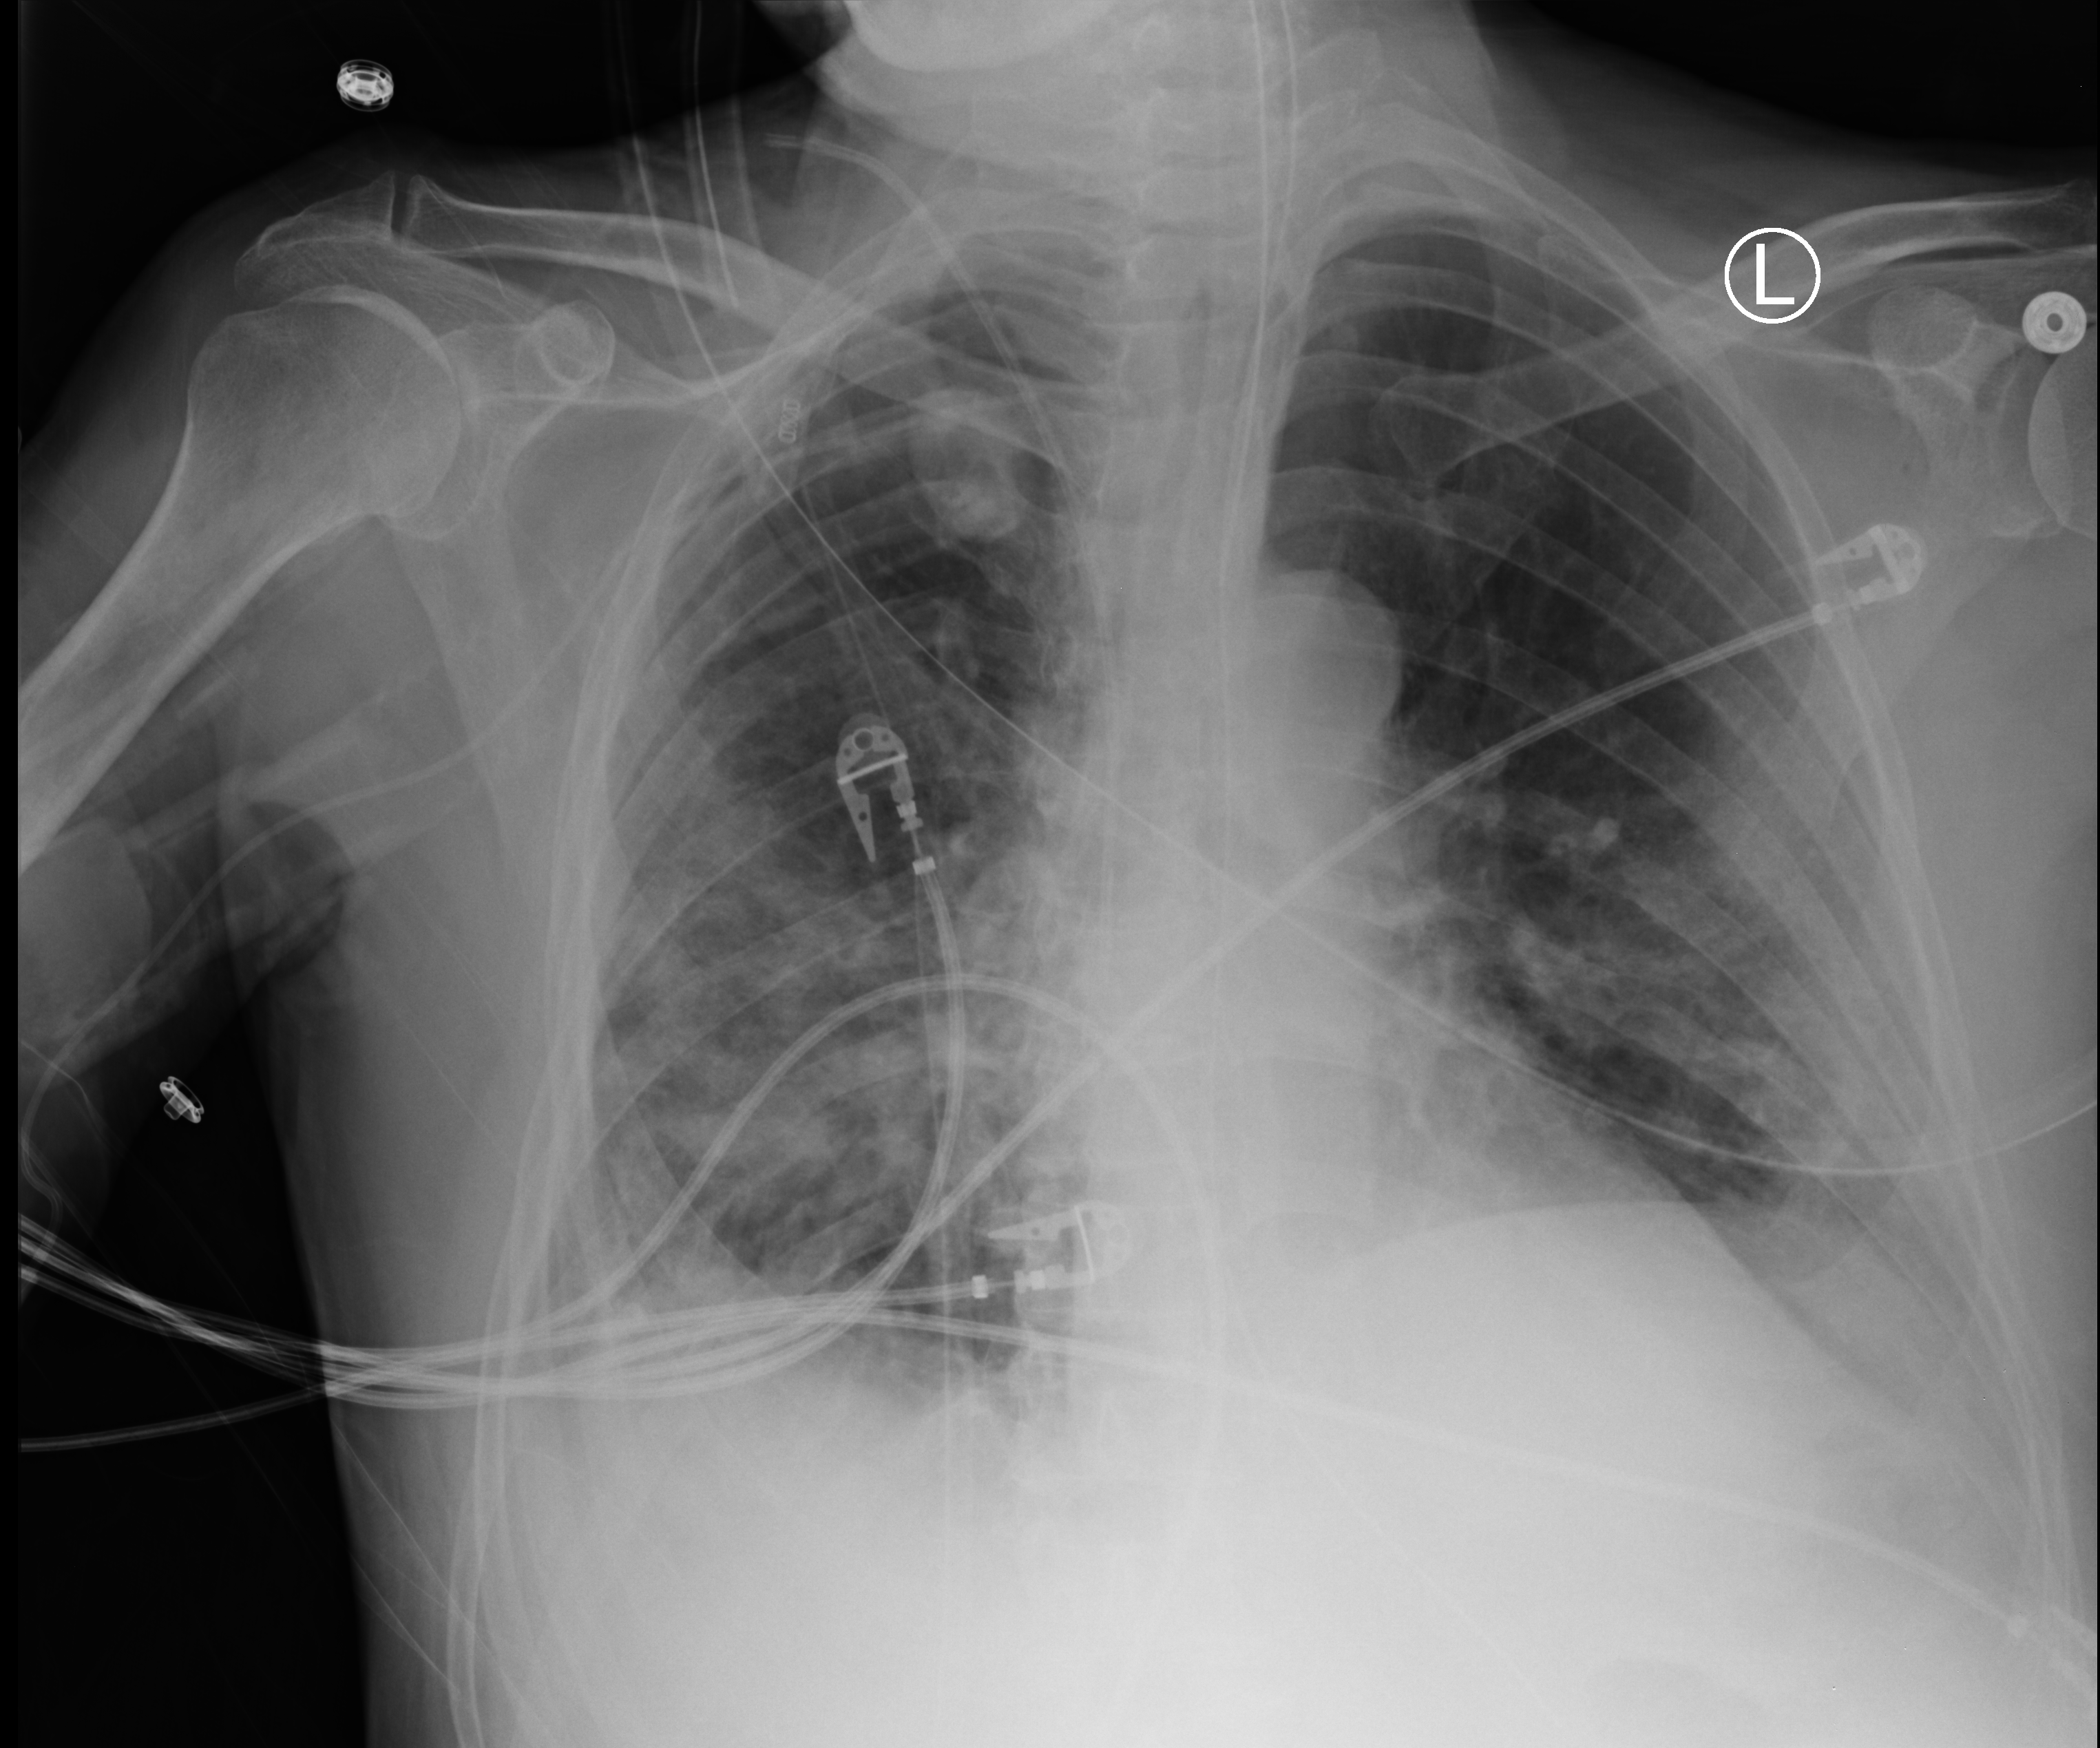
Bedside chest radiograph (computed radiography), anteroposterior (AP) projection. Male patient hospitalised with COVID-19, age 75–90 years.
Admission-level facts for this patient (not findings on this image; timing relative to this image not recorded):
- mechanically ventilated during this hospital stay: yes
- length of hospital stay: 70 days